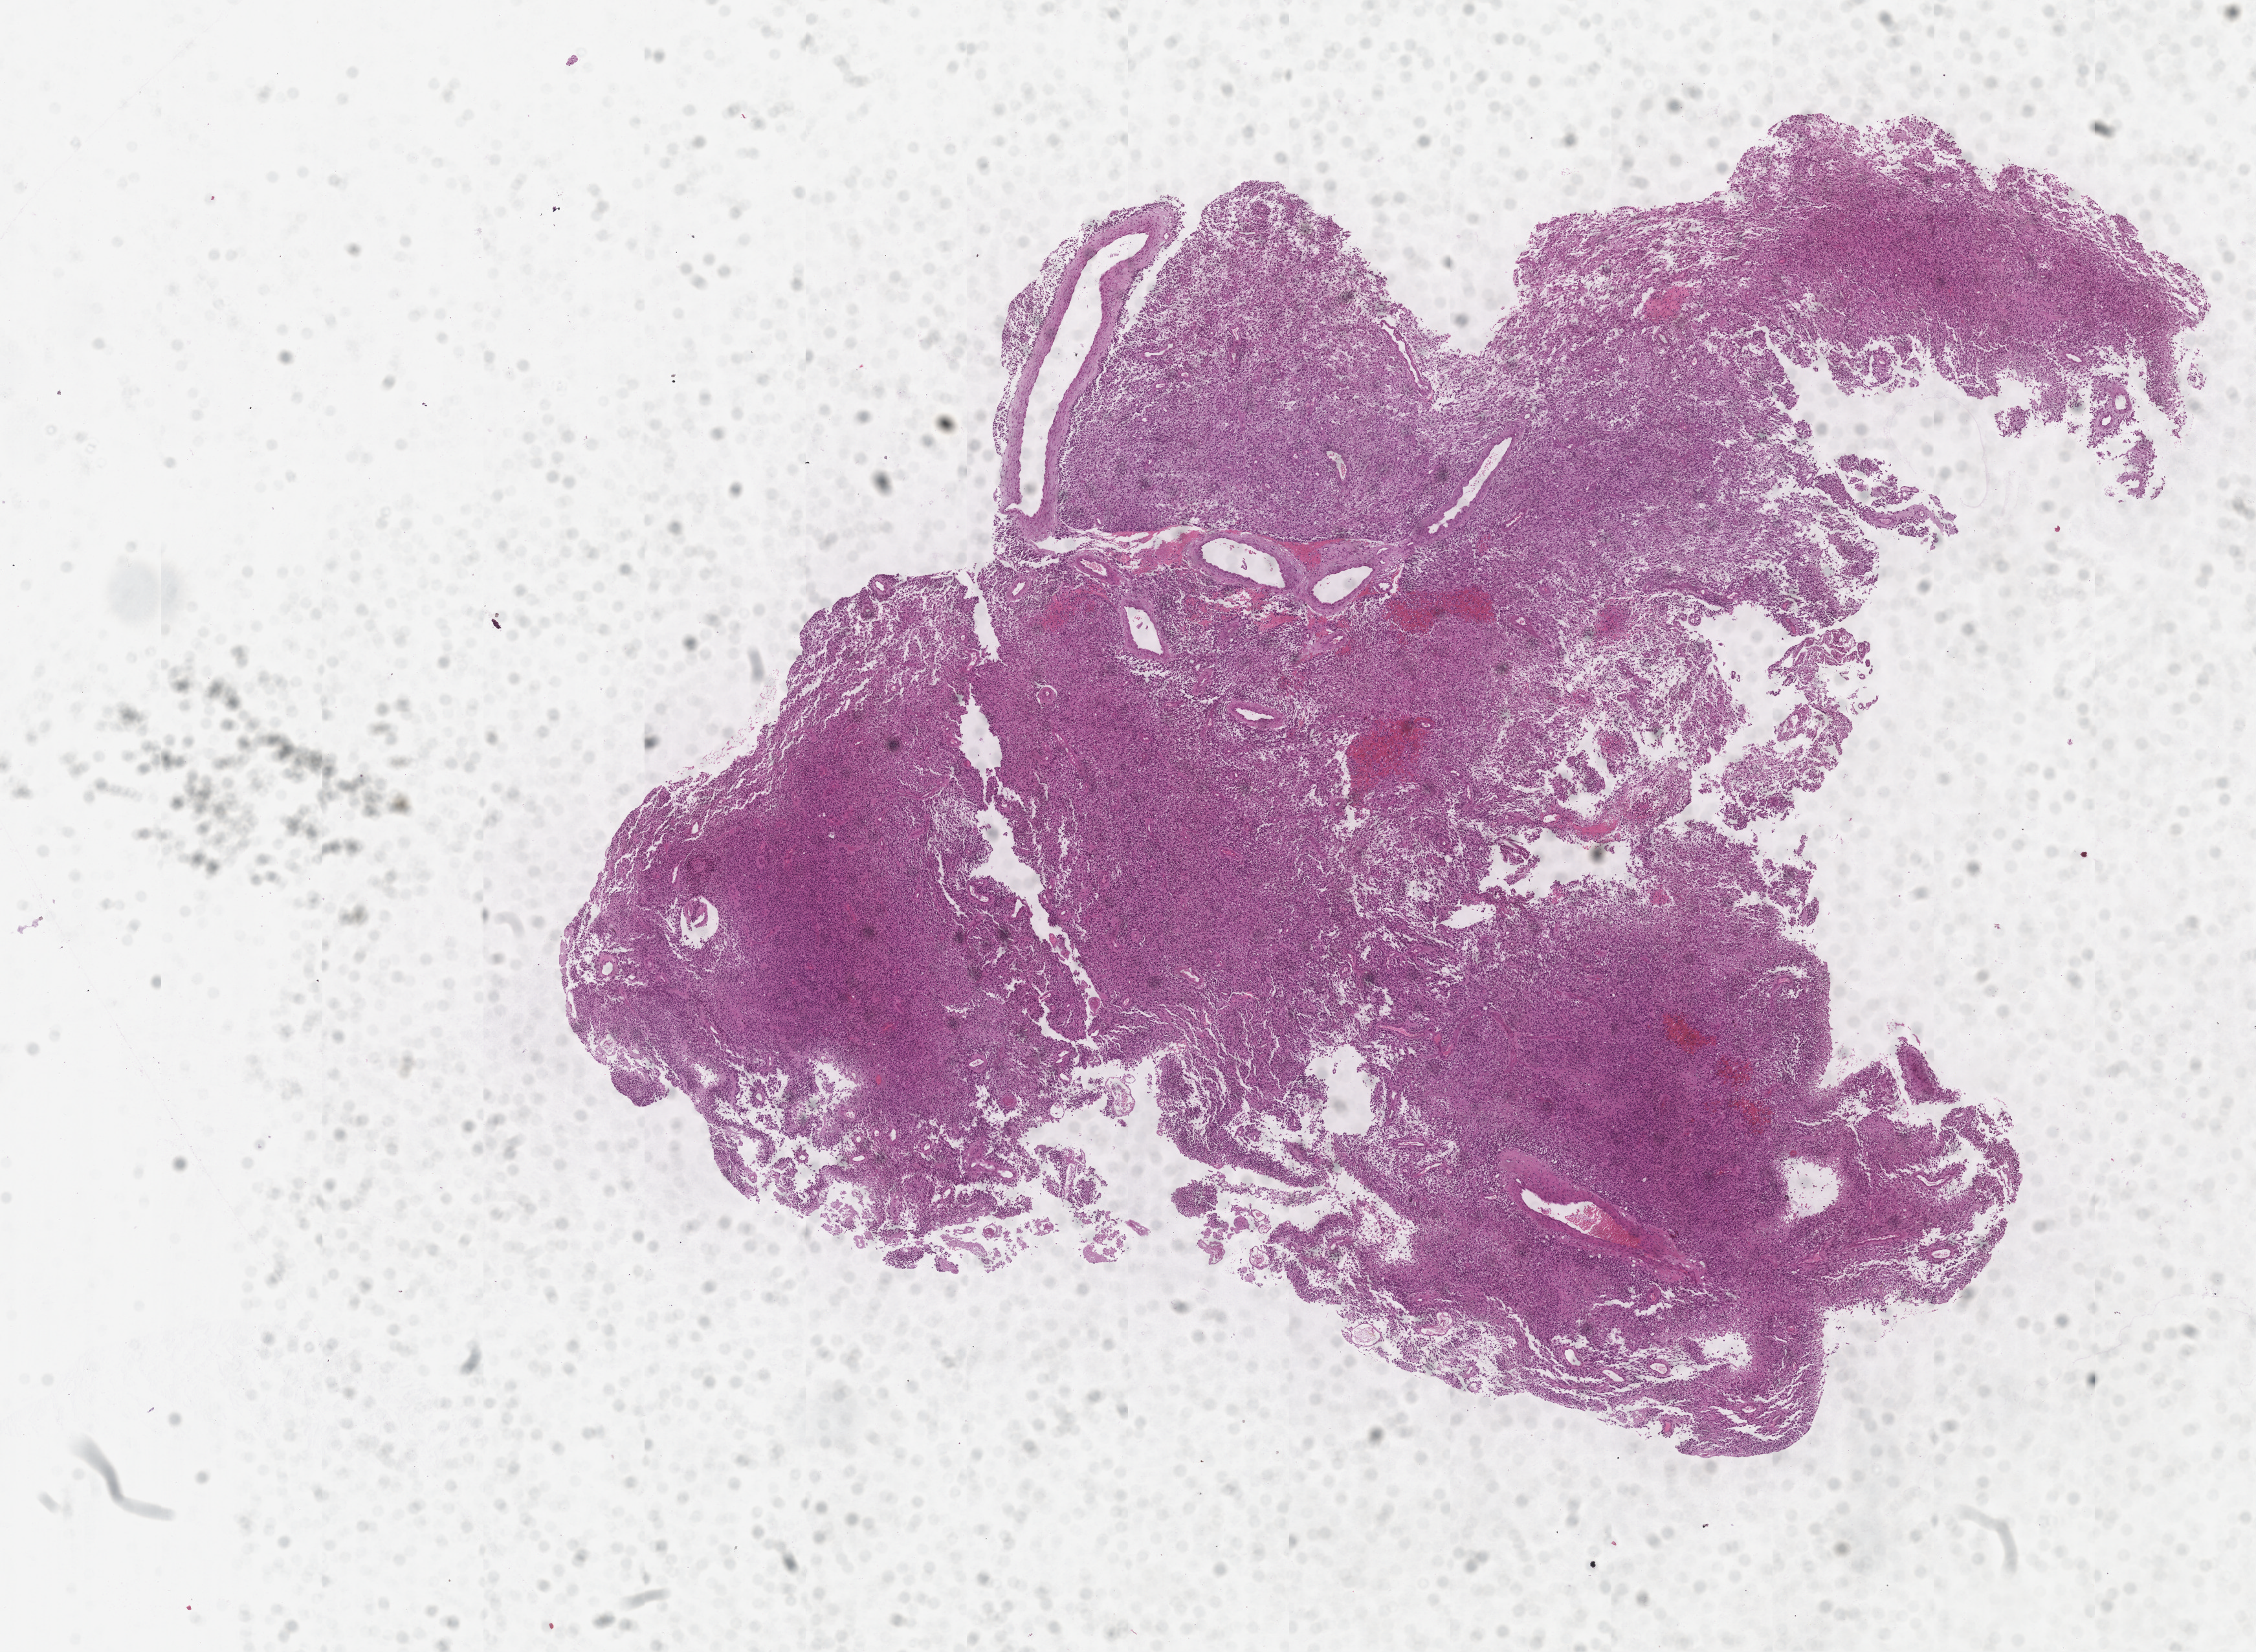
Digitized H&E tissue section (whole slide), whole scanned area (about 14.0 x 10.3 mm) shown as a low-resolution overview, tumour tissue sample, sampled site: brain. Patient: female, age 63 years. Pathologist review of this section (percent, as recorded): tumour nuclei 80%, necrosis 5%.
Diagnosis: Glioblastoma.